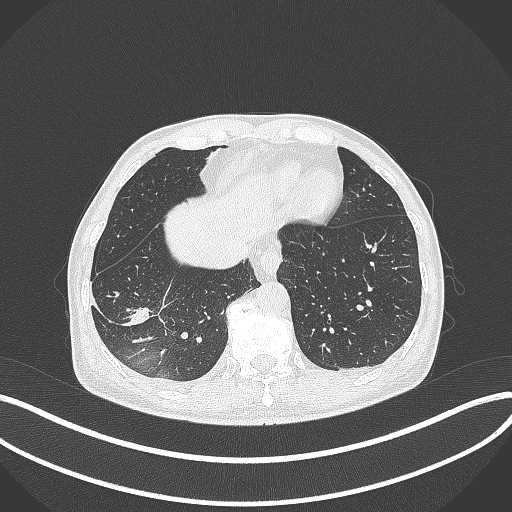
Chest CT, one axial slice. Position 88 of 388 along the scan axis. Lung window (W 1500 / L -600 HU). 512 × 512 image matrix, field of view 400 × 400 mm. Patient: male, 64 years. From the clinical record (not read from this slice): clinical TNM (as recorded): T3 N0 M0; histopathological grade: G2-3.
Annotated regions visible in this slice (bounding box drawn by a radiologist):
- lung tumour (recorded histology: adenocarcinoma): bounding box (x1, y1, x2, y2) in pixels: (120, 300, 154, 332)